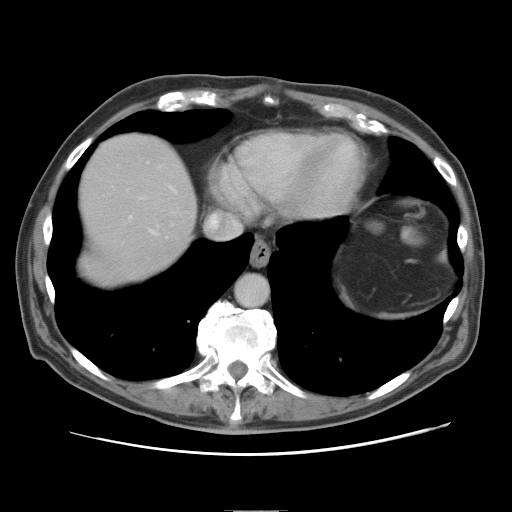
Contrast-enhanced abdominal CT, one axial slice; position 72 of 89 along the scan axis; 120 kVp; soft-tissue window (W 400 / L 40 HU); 512 × 512 image matrix, field of view 375 × 375 mm. Male patient, age 69 years. From the clinical record (not read from this slice): diagnosis: colorectal cancer liver metastases, imaged before liver resection; multiple liver metastases: no; largest metastasis: 8.5 cm.
Annotated regions visible in this slice (expert manual segmentation):
- hepatic veins: bounding box <142,198,156,234> (left, top, right, bottom; pixels)
- liver: <80,134,196,287>
- planned liver remnant (the part of the liver to remain after resection): <79,134,197,287>
- portal vein (with intrahepatic branches): <129,216,132,220>